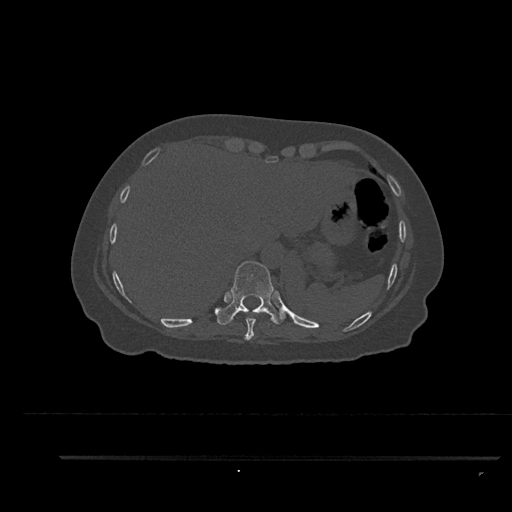
CT including the spine, one axial slice; position 380 of 797 along the scan axis; reconstruction kernel Br40s/3; bone window (W 1800 / L 400 HU); 0.5 mm slice thickness; 512 × 512 image matrix, field of view 408 × 408 mm. Patient: female, 44 years. Case-level facts recorded for this patient, not image findings: primary cancer: renal.
Outlined on this slice (semi-automatically segmented with operator editing):
- T10 vertebra: bounding box [x1, y1, x2, y2] px = [217, 261, 284, 325]
- T9 vertebra: [244, 308, 256, 340]